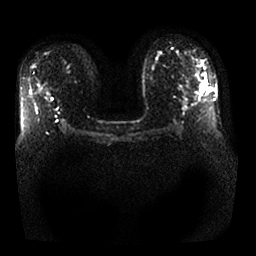
Breast MRI, one axial slice; position 16 of 25 along the scan axis; diffusion-weighted series; image 2 of 4 stored at this slice position (different b-values; order by instance number); 1.5 T; 4 mm slice thickness; 256 × 256 image matrix. Female patient.
Structures marked on this image (outlined manually by an expert reader):
- tumour on diffusion-weighted imaging: box from (x=201, y=79) to (x=206, y=92) px